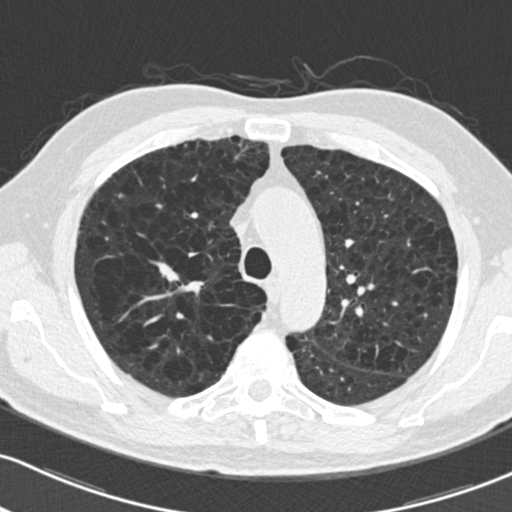
Low-dose screening chest CT, one axial slice; reconstruction kernel B30f; 120 kVp; lung window (W 1500 / L -600 HU); 2 mm slice thickness; 512 × 512 image matrix, field of view 318 × 318 mm.
Annotated regions visible in this slice (expert manual segmentation):
- lesion 1 (tumor, upper lobe of right lung): bounding box <152,262,179,282> (left, top, right, bottom; pixels)